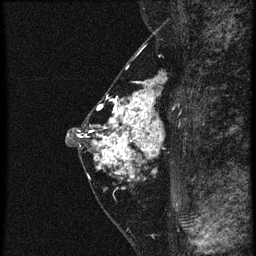
Breast MRI (dynamic contrast-enhanced), one sagittal slice. Slice 29 of 60 in the series (ordered by position). 4 images stored at this slice position (order not interpretable as contrast timing). 1.5 T. TE 4.2 ms, TR 20.4 ms. 1.5 mm slice thickness. 256 × 256 image matrix, field of view 180 × 180 mm. Patient: female, 46 years. Case-level facts recorded for this patient, not image findings: setting: breast cancer imaged before/during neoadjuvant chemotherapy; receptor status: triple-negative.
Structures marked on this image (semi-automatically segmented with operator editing):
- analysis volume of interest (the breast-tissue region the enhancement analysis was run in; not a lesion): bounding box (x1, y1, x2, y2) in pixels: (88, 82, 173, 185)
- tumour enhancement mask (voxels above the 90 % enhancement threshold inside the analysis volume of interest): (92, 82, 163, 177)